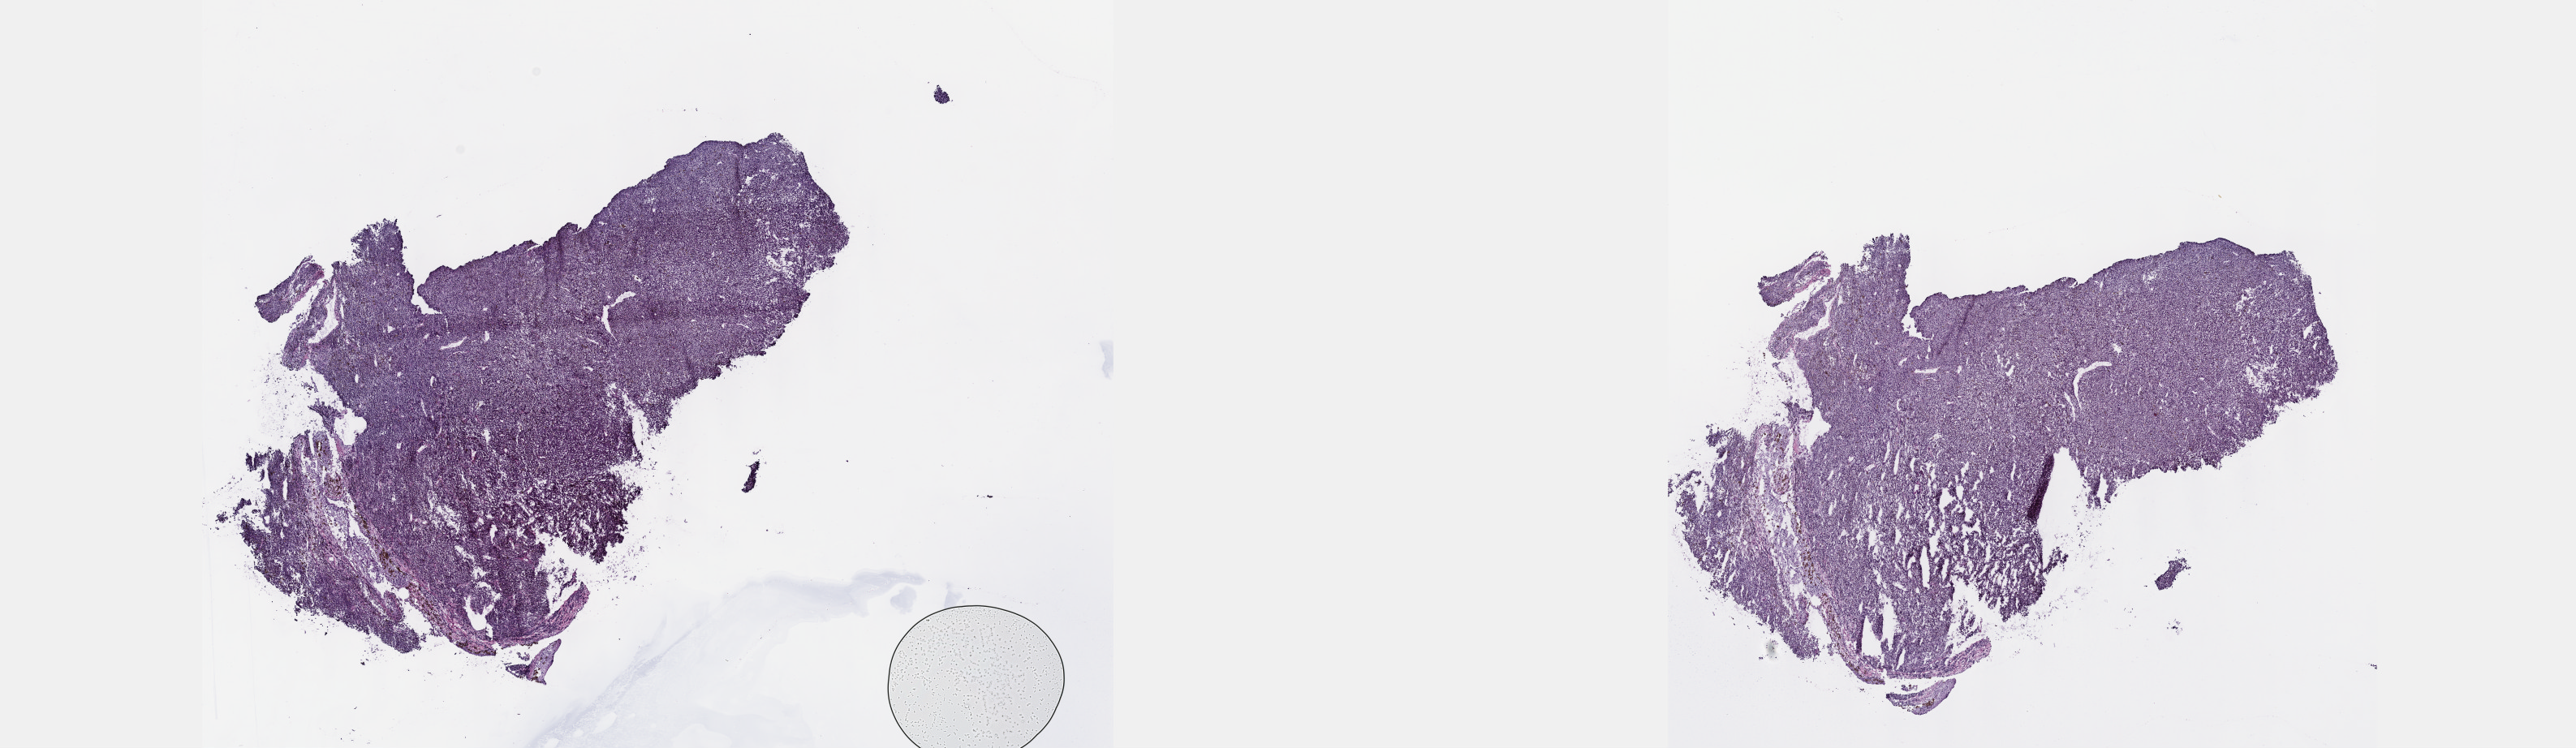
H&E whole-slide image, a low-resolution overview of the entire scanned area, about 25.7 x 7.5 mm; frozen section from the top of the tissue portion; primary tumour sample from the uvea. Male patient; age at initial diagnosis 38 years. Slide review estimates, as recorded: tumour cells 95%, tumour nuclei 80%, normal cells 0%, stromal cells 0%, necrosis 5%. Infiltration values recorded for this section: lymphocyte infiltration 2%, monocyte infiltration 0%, neutrophil infiltration 0%.
• pathologic diagnosis: Spindle cell melanoma, NOS (choroid)
• AJCC pathologic stage: IIB